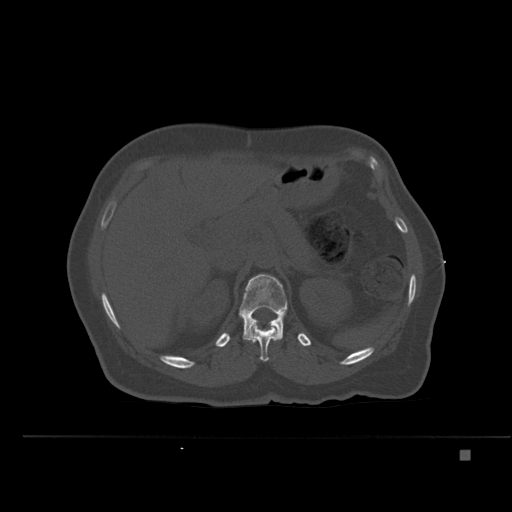
CT including the spine, one axial slice; slice 244 of 477 in the series (ordered by position); bone window (W 1800 / L 400 HU); 1.5 mm slice thickness; 512 × 512 image matrix. Patient: female, 74 years. From the clinical record (not read from this slice): primary cancer: colon.
Outlined on this slice (semi-automatic segmentation, software-assisted and operator-edited):
- L1 vertebra: bounding box (x1, y1, x2, y2) in pixels: (239, 274, 288, 340)
- T12 vertebra: (250, 321, 277, 362)